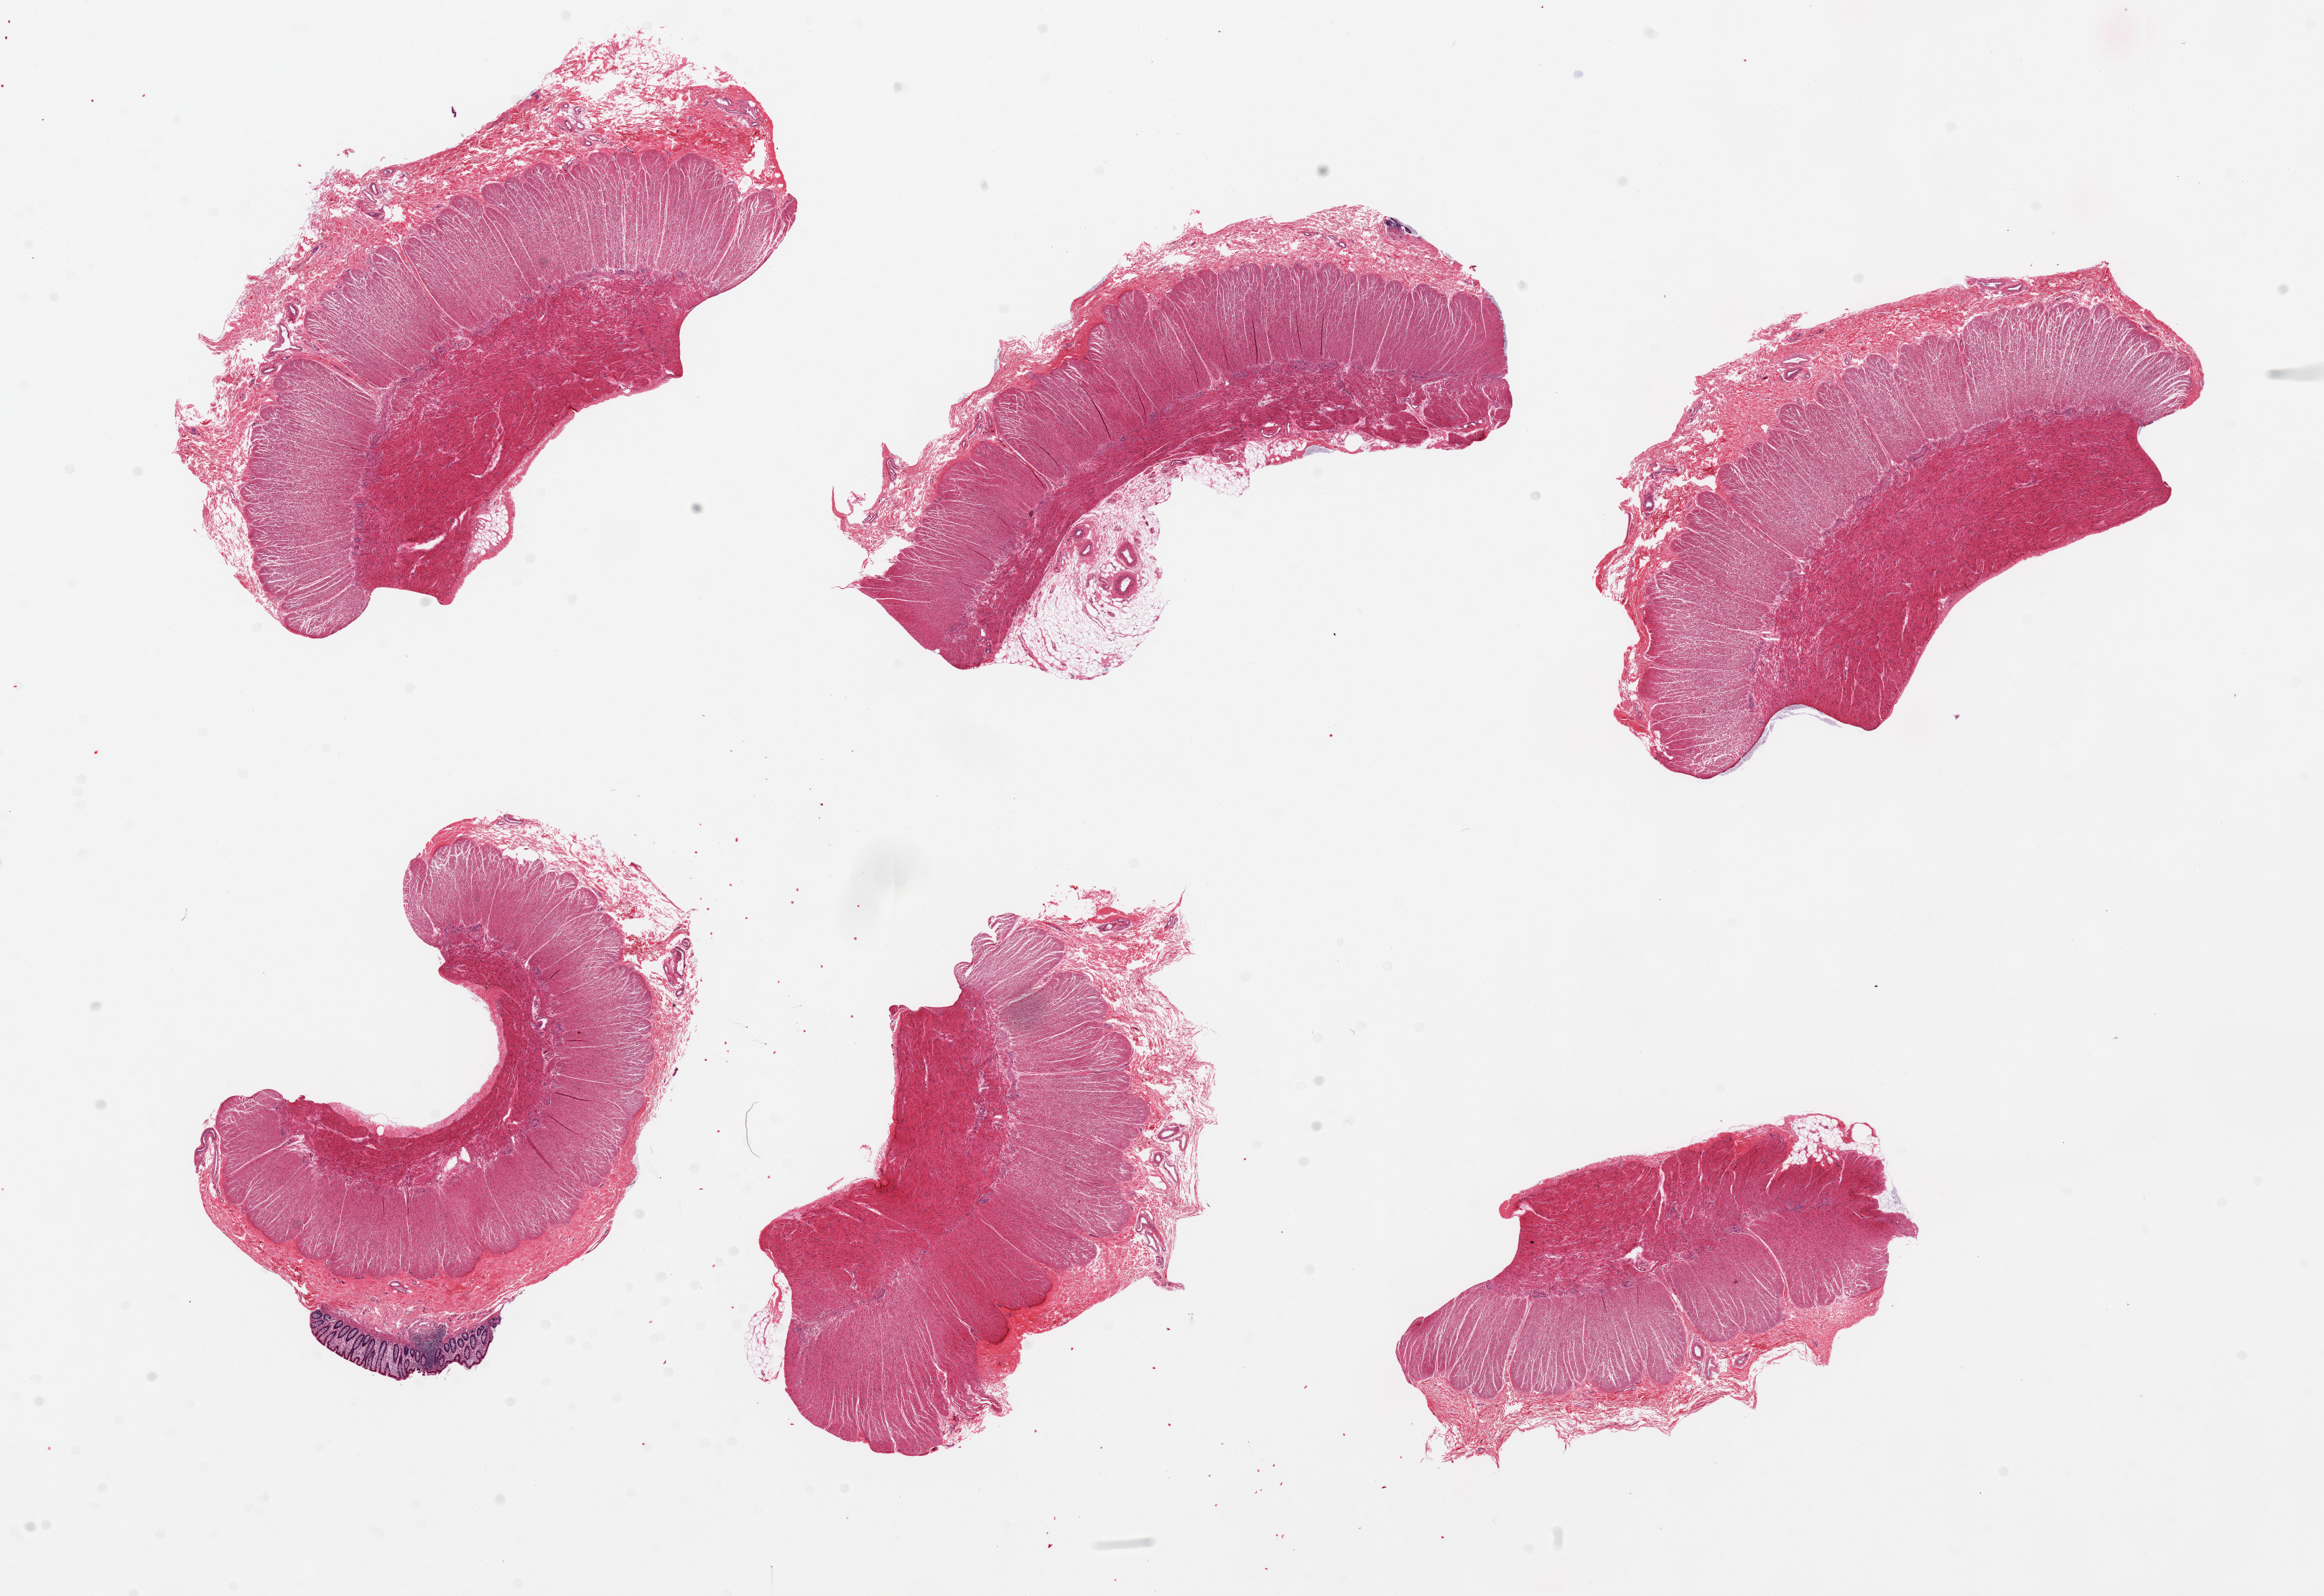
Whole-slide image, H&E stain — a low-resolution overview of the entire scanned area, about 25.6 x 17.6 mm. PAXgene-fixed paraffin-embedded (PFPE) section. Sampled site (target tissue): sigmoid colon. Donor tissue sample. Donor sex: female.
Review note (as recorded): 6 pieces, predominantly muscularis with small strip of mucosa, attachment of fat.